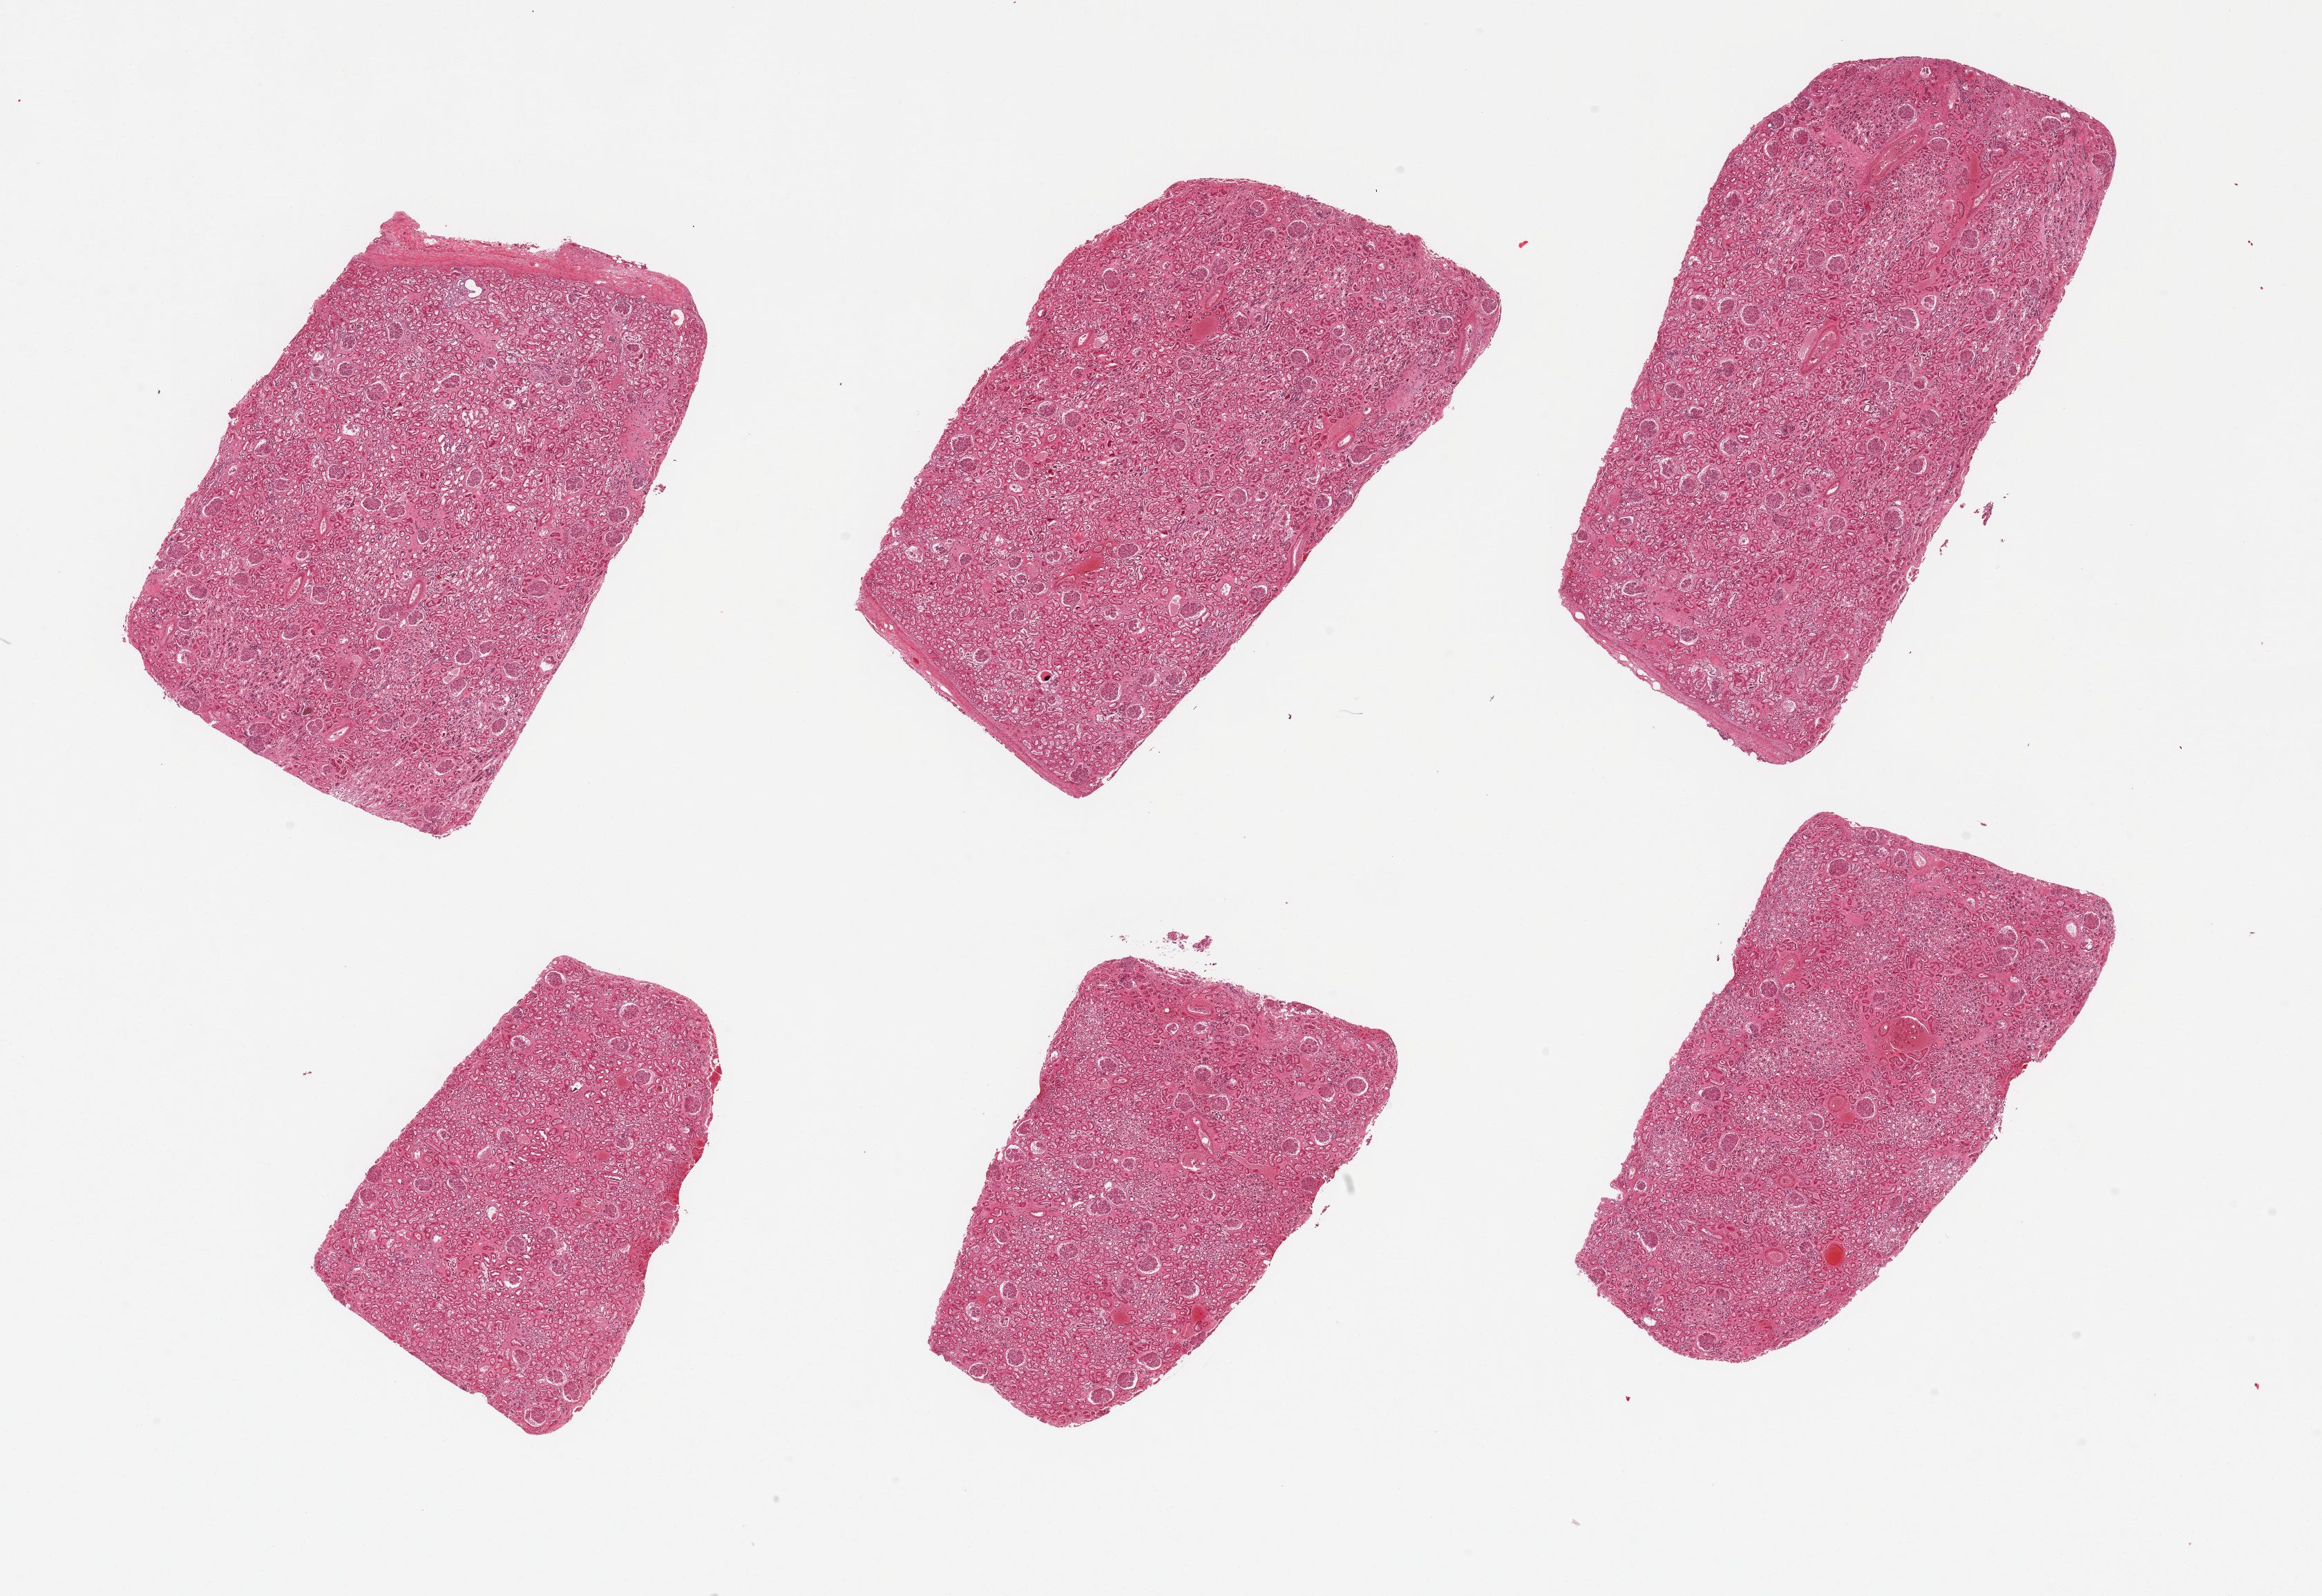
Whole-slide image, H&E stain — whole scanned area (about 26.6 x 18.3 mm) shown as a low-resolution overview. PAXgene-fixed paraffin-embedded (PFPE) section. Sampled site (target tissue): renal cortex. Donor tissue sample. Donor sex: male.
* review note (as recorded): 6 pieces, glomeruli present, tubules with moderately advanced autolysis